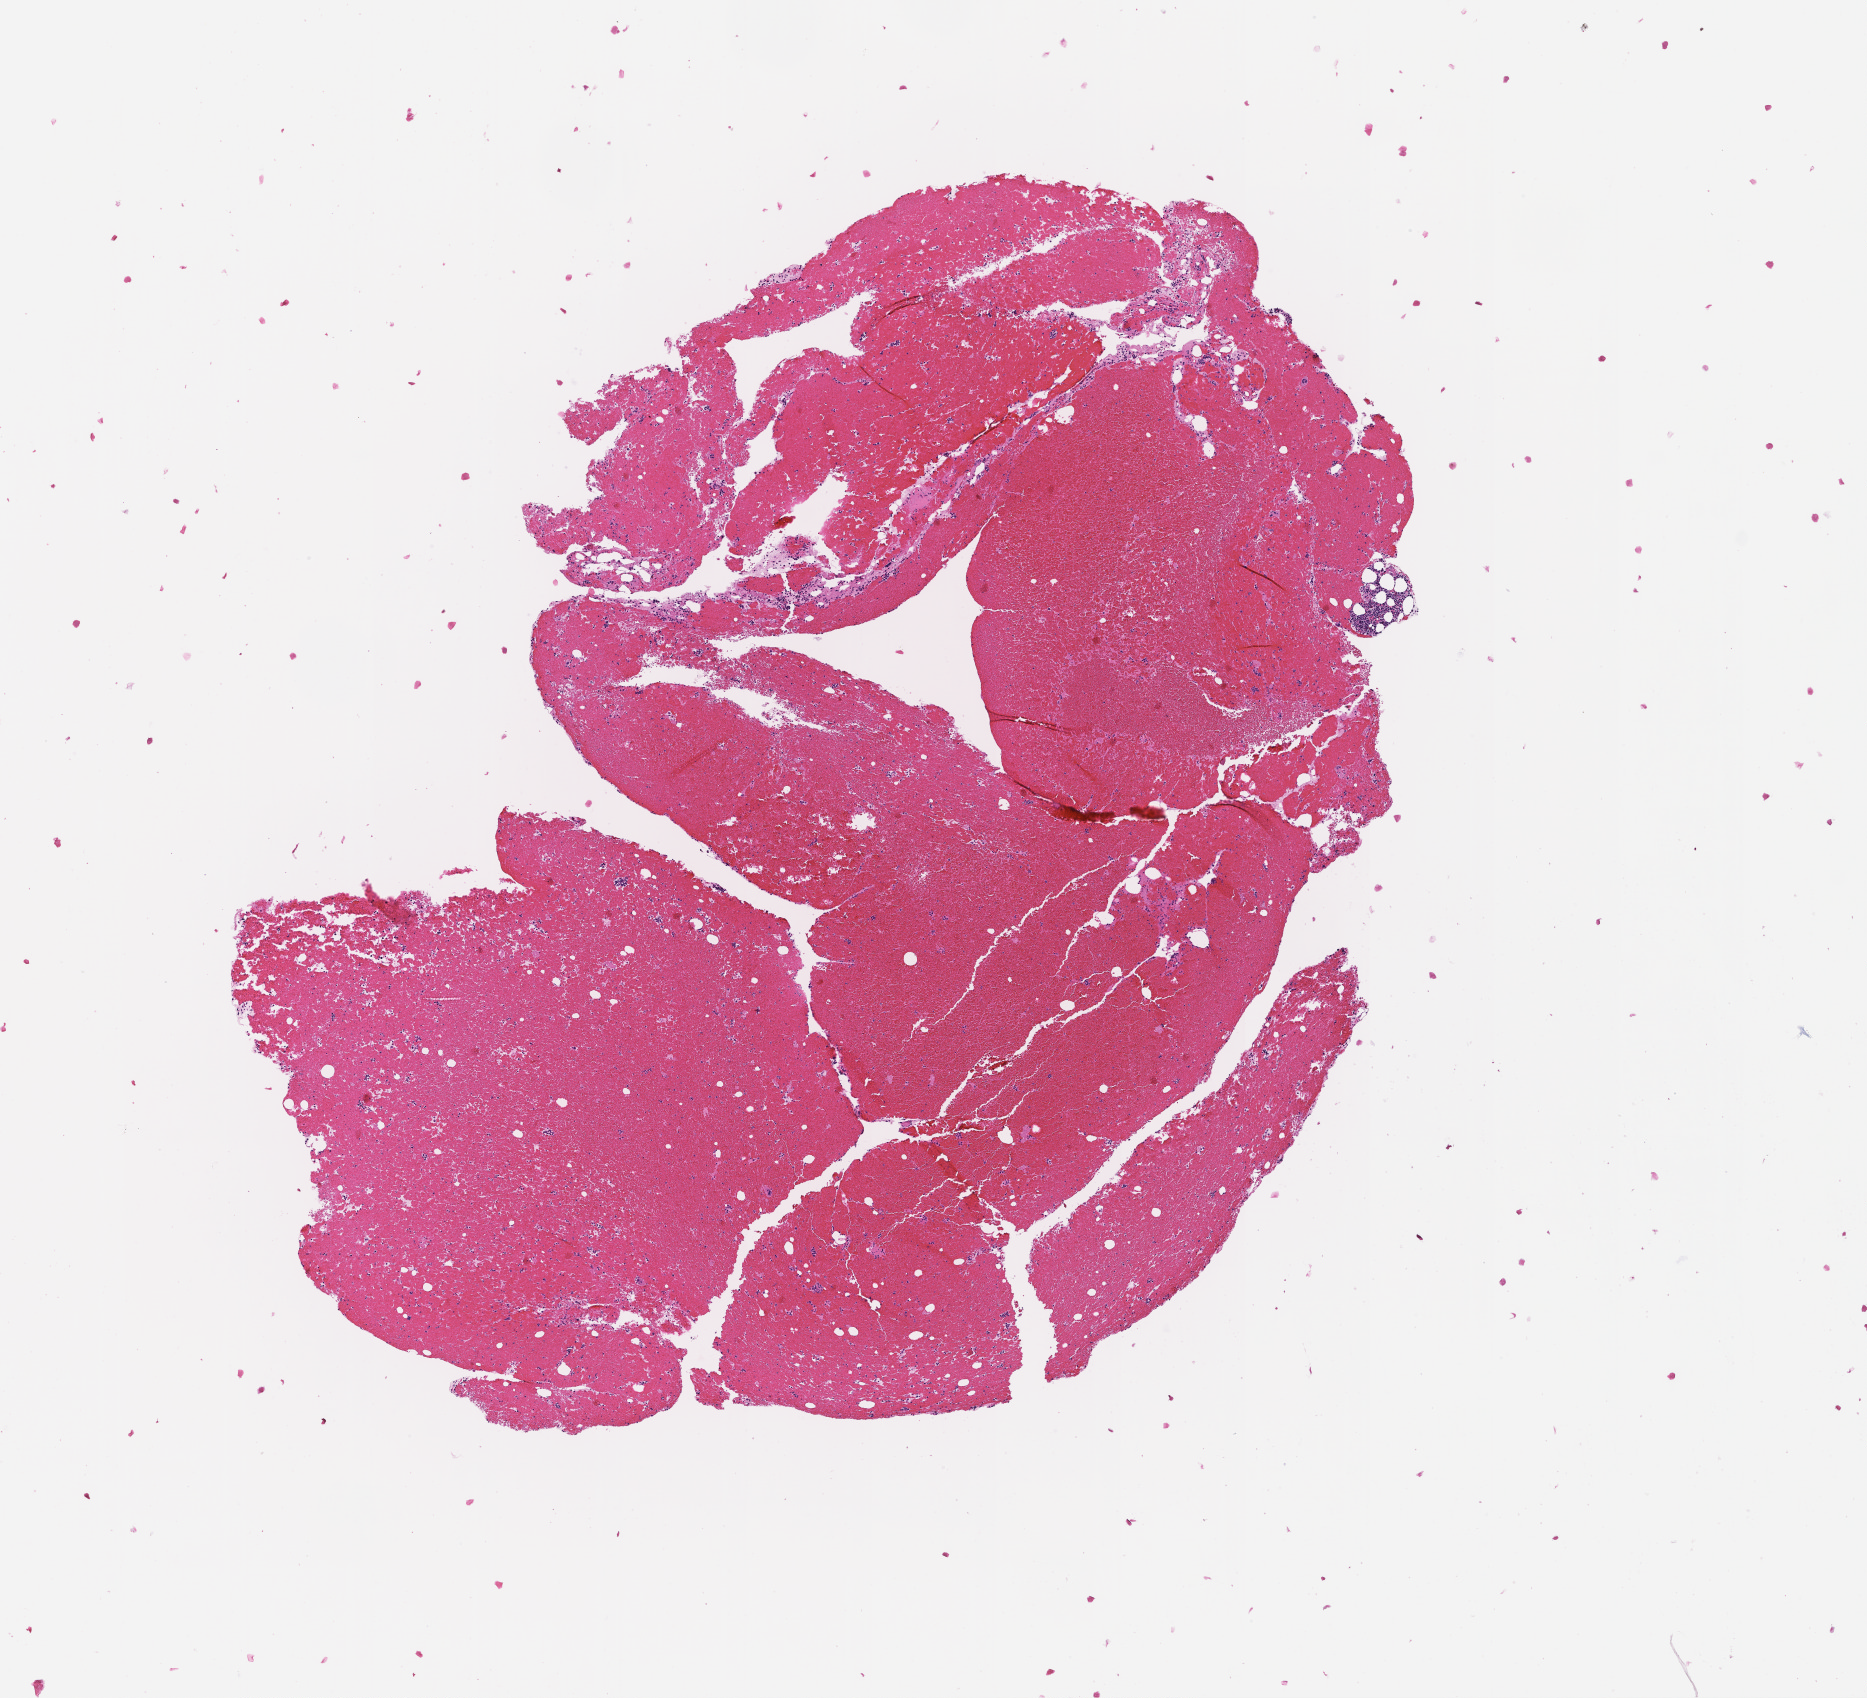
Haematoxylin and eosin whole-slide image, whole scanned area (about 7.5 x 6.9 mm) shown as a low-resolution overview; formalin-fixed paraffin-embedded section; site: bone marrow; archival tissue. Male patient.
This section: primary tumour tissue. Diagnosis: Plasma Cell Myeloma.